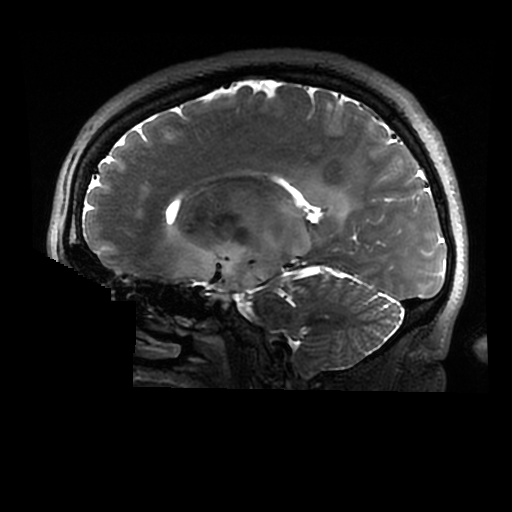
Brain MRI from a brain-tumour surgery series, one sagittal slice. Position 176 of 320 along the scan axis. 512 × 512 image matrix, field of view 240 × 240 mm. From the clinical record (not read from this slice): histopathology: Astrocytoma; WHO grade: 2; IDH mutation: yes.
Outlined on this slice (expert manual segmentation):
- tumour: box from (x=200, y=198) to (x=349, y=304) px